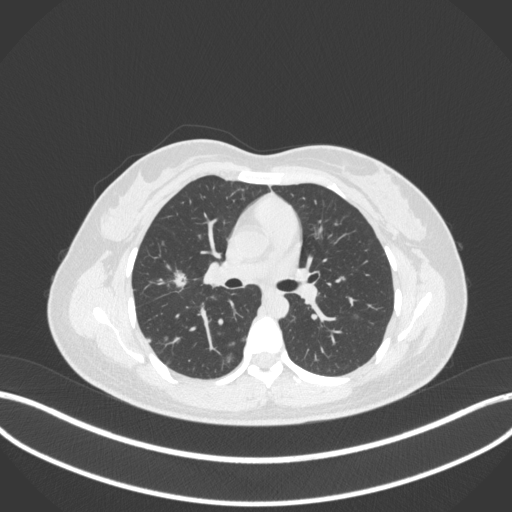
Chest CT, one axial slice. Slice 196 of 214 in the series (ordered by position). Reconstruction kernel B31f. 120 kVp. Lung window (W 1500 / L -600 HU). 512 × 512 image matrix. Female patient, age 33 years. From the clinical record (not read from this slice): clinical TNM (as recorded): T1c N0 M0.
Annotated regions visible in this slice (rectangle marked by the reading radiologist):
- lung tumour (recorded histology: adenocarcinoma): bounding box [x1, y1, x2, y2] px = [169, 268, 191, 296]